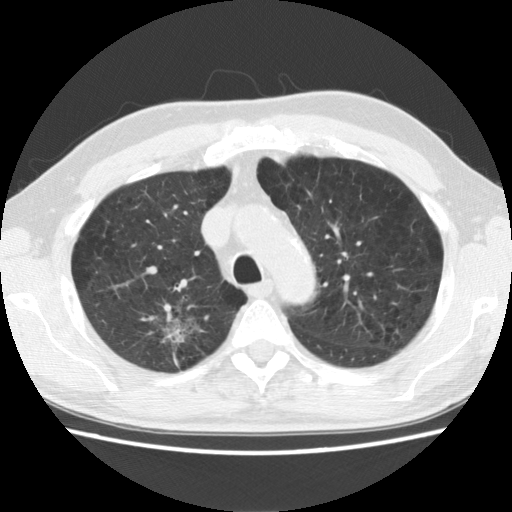
Chest CT (low-dose screening protocol), one axial image, baseline annual screen, lung window (W 1500 / L -600 HU), slice 40 of 142 in the series, 512 × 512 image matrix. Male participant, aged 64 years at enrolment. Former smoker at enrolment.
- Expert-annotated lung lesion, bounding box [x1, y1, x2, y2] px = [118, 297, 208, 367].
- Reader record for this screening exam (exam-level; its link to the box is not recorded): non-calcified nodule or mass ≥4 mm, right upper lobe, 39 × 31 mm, spiculated (stellate) margins, mixed attenuation.
- Official screen result: positive, change unspecified: nodule(s) >= 4 mm or enlarging nodule(s), mass(es), or other non-specific abnormalities suspicious for lung cancer.
- Later outcome: lung cancer diagnosed 74 days after this screen — adenocarcinoma, NOS, right upper lobe, moderately differentiated (G2), stage IB (AJCC 6th edition), 40 mm at pathology.